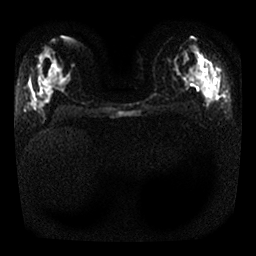
Breast MRI, one axial slice; slice 16 of 25 in the series (ordered by position); diffusion-weighted series; image 2 of 4 stored at this slice position (different b-values; order by instance number); 1.5 T; 4 mm slice thickness; 256 × 256 image matrix, field of view 320 × 320 mm. Female patient.
Outlined on this slice (outlined manually by an expert reader):
- tumour on diffusion-weighted imaging: bounding box <208,64,215,83> (left, top, right, bottom; pixels)